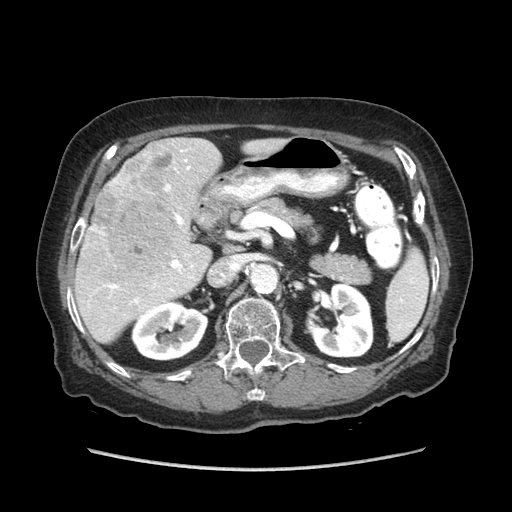
Contrast-enhanced abdominal CT (liver protocol), one axial slice. Position 38 of 89 along the scan axis. Reconstruction kernel STANDARD. Soft-tissue window (W 400 / L 40 HU). 2.5 mm slice thickness. 512 × 512 image matrix, field of view 360 × 360 mm. Case-level facts recorded for this patient, not image findings: diagnosis: hepatocellular carcinoma (patient treated with transarterial chemoembolisation; whether this scan precedes or follows treatment is not stated here); TNM stage (as recorded): Stage-IIIA; Child-Pugh class: A; tumour differentiation: well differentiated; tumour nodularity: multinodular.
Annotated regions visible in this slice (semi-automatically segmented with operator editing):
- liver parenchyma outside the tumour (the mass and vessels are separate outlines, so this box may not span the whole liver): box from (x=74, y=138) to (x=285, y=342) px
- mass: (x=92, y=143)–(x=180, y=276)
- liver vessels: (x=90, y=150)–(x=193, y=304)